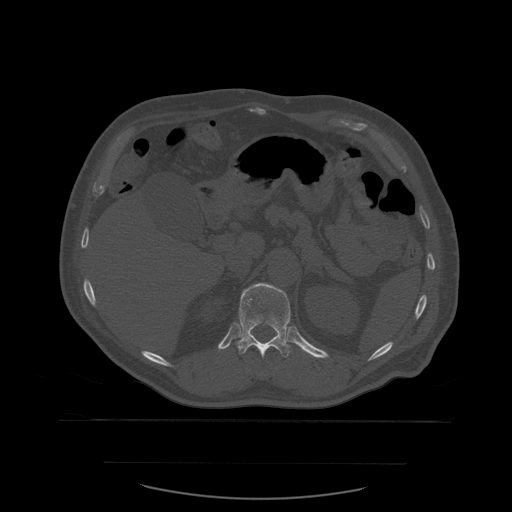
CT including the spine, one axial slice; position 273 of 590 along the scan axis; bone window (W 1800 / L 400 HU); 512 × 512 image matrix. Patient age 71 years. Case-level facts recorded for this patient, not image findings: primary cancer: lung.
Outlined on this slice (semi-automatic segmentation, software-assisted and operator-edited):
- T12 vertebra: bounding box <236,283,292,375> (left, top, right, bottom; pixels)